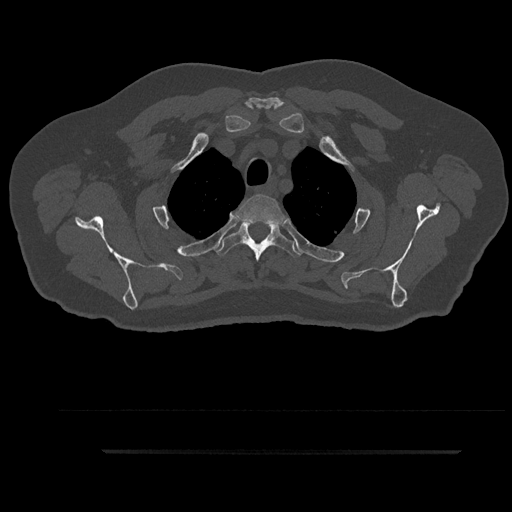
CT including the spine, one axial slice. Position 732 of 797 along the scan axis. 120 kVp. Bone window (W 1800 / L 400 HU). 512 × 512 image matrix. Patient: male, 63 years. Case-level facts recorded for this patient, not image findings: primary cancer: renal; vertebrae with lytic lesions (as recorded): T8.
Outlined on this slice (semi-automatic segmentation, software-assisted and operator-edited):
- T2 vertebra: bounding box [x1, y1, x2, y2] px = [236, 194, 285, 224]
- T3 vertebra: [215, 221, 302, 262]